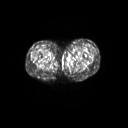
FDG PET of an extremity soft-tissue mass (from a PET/CT study), one axial slice; slice 33 of 267 in the series (ordered by position); 3.27 mm slice thickness; 128 × 128 image matrix, field of view 600 × 600 mm. Patient: female, 24 years. From the clinical record (not read from this slice): histological type: leiomyosarcoma; grade: high; site of the primary tumour: groin.
Outlined on this slice (expert contour drawn on MRI and transferred to this co-registered scan by the dataset authors):
- gross tumour volume including surrounding oedema: bounding box (x1, y1, x2, y2) in pixels: (62, 58, 69, 62)